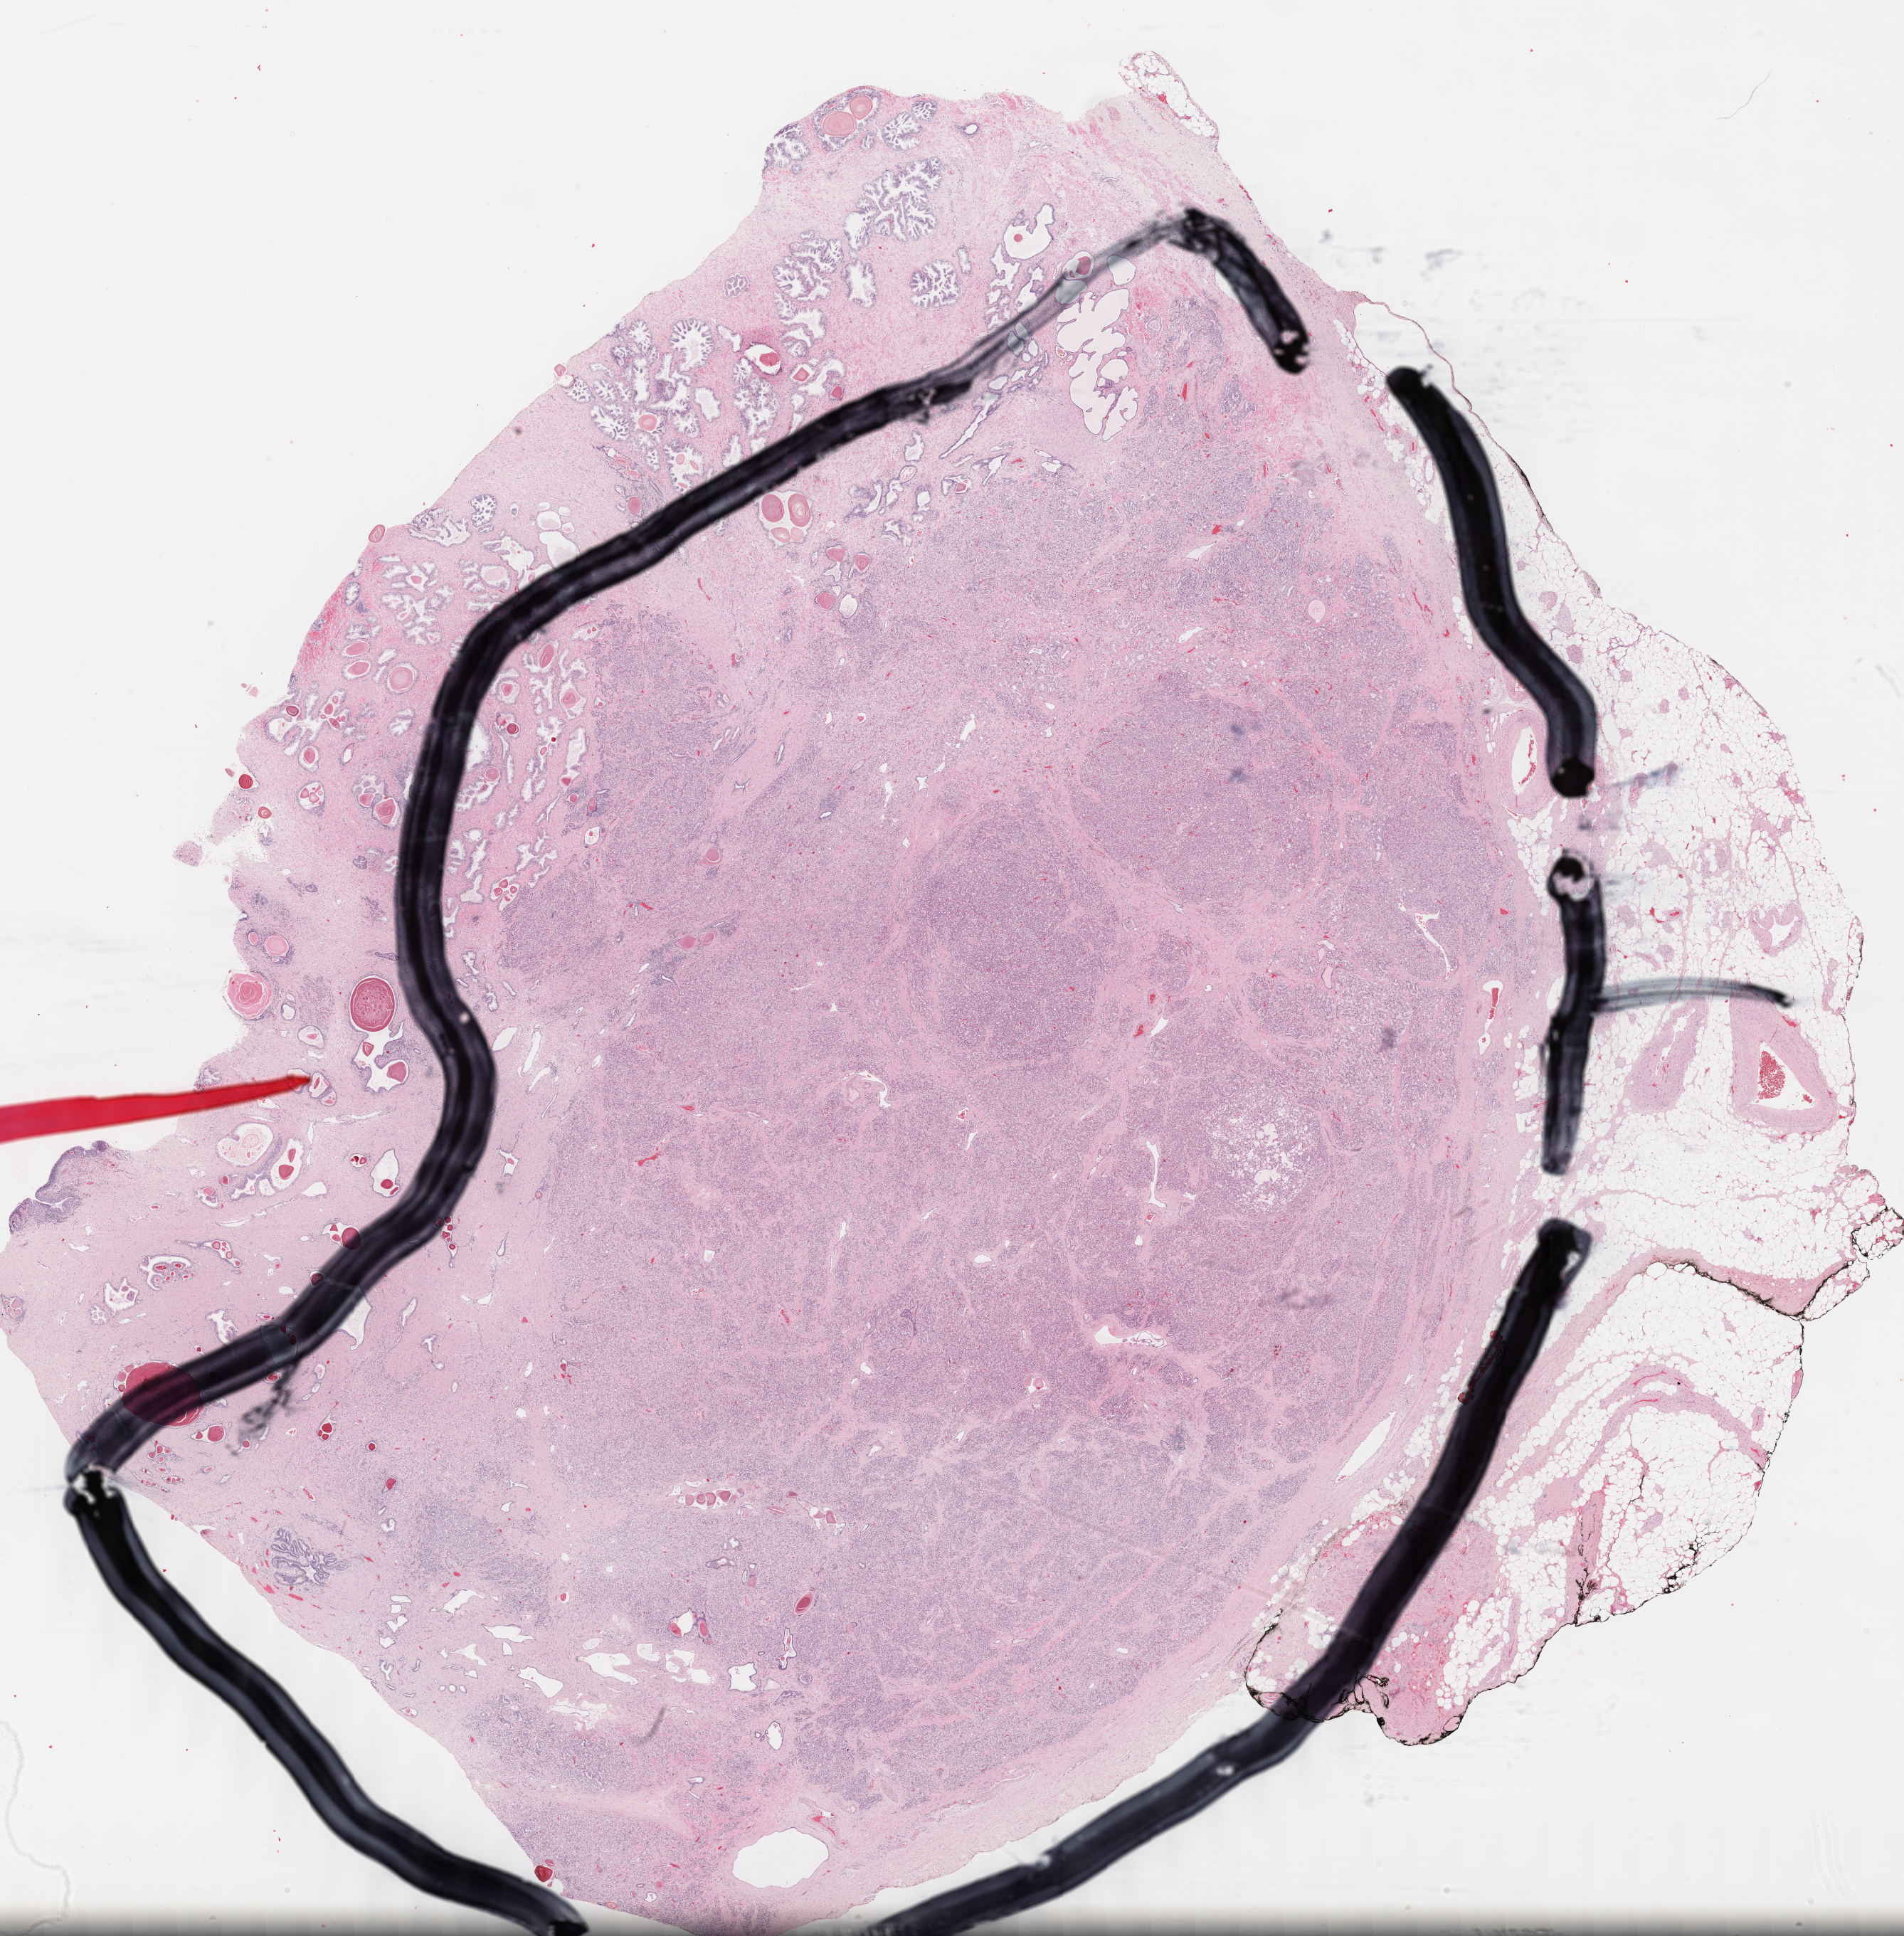
H&E whole-slide image, shown as a low-resolution overview of the whole scanned area (about 21.3 x 21.6 mm, acquisition: 40x scan); formalin-fixed paraffin-embedded (FFPE) diagnostic section; prostate, primary tumour sample. Patient: male, age at initial diagnosis 64 years. Gleason score: 9 (4+5).
Pathologic diagnosis: Adenocarcinoma, NOS (prostate gland). Laterality: bilateral. Lymph nodes positive (case pathology): 0 of 6 examined.